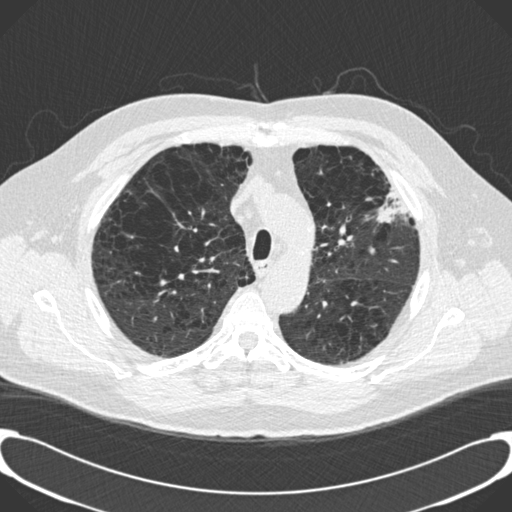
Axial slice from a low-dose chest CT screening exam, third annual screen, lung window (W 1500 / L -600 HU), 2 mm slice thickness, 512 × 512 image matrix. Male, age 59 years at enrolment. Current smoker at enrolment.
• Lesion marked by an expert reader, bounding box (x1, y1, x2, y2) in pixels: (360, 162, 414, 225).
• No non-calcified nodule or mass ≥4 mm was recorded by the screening reader at this exam.
• Official screen result: positive, other.